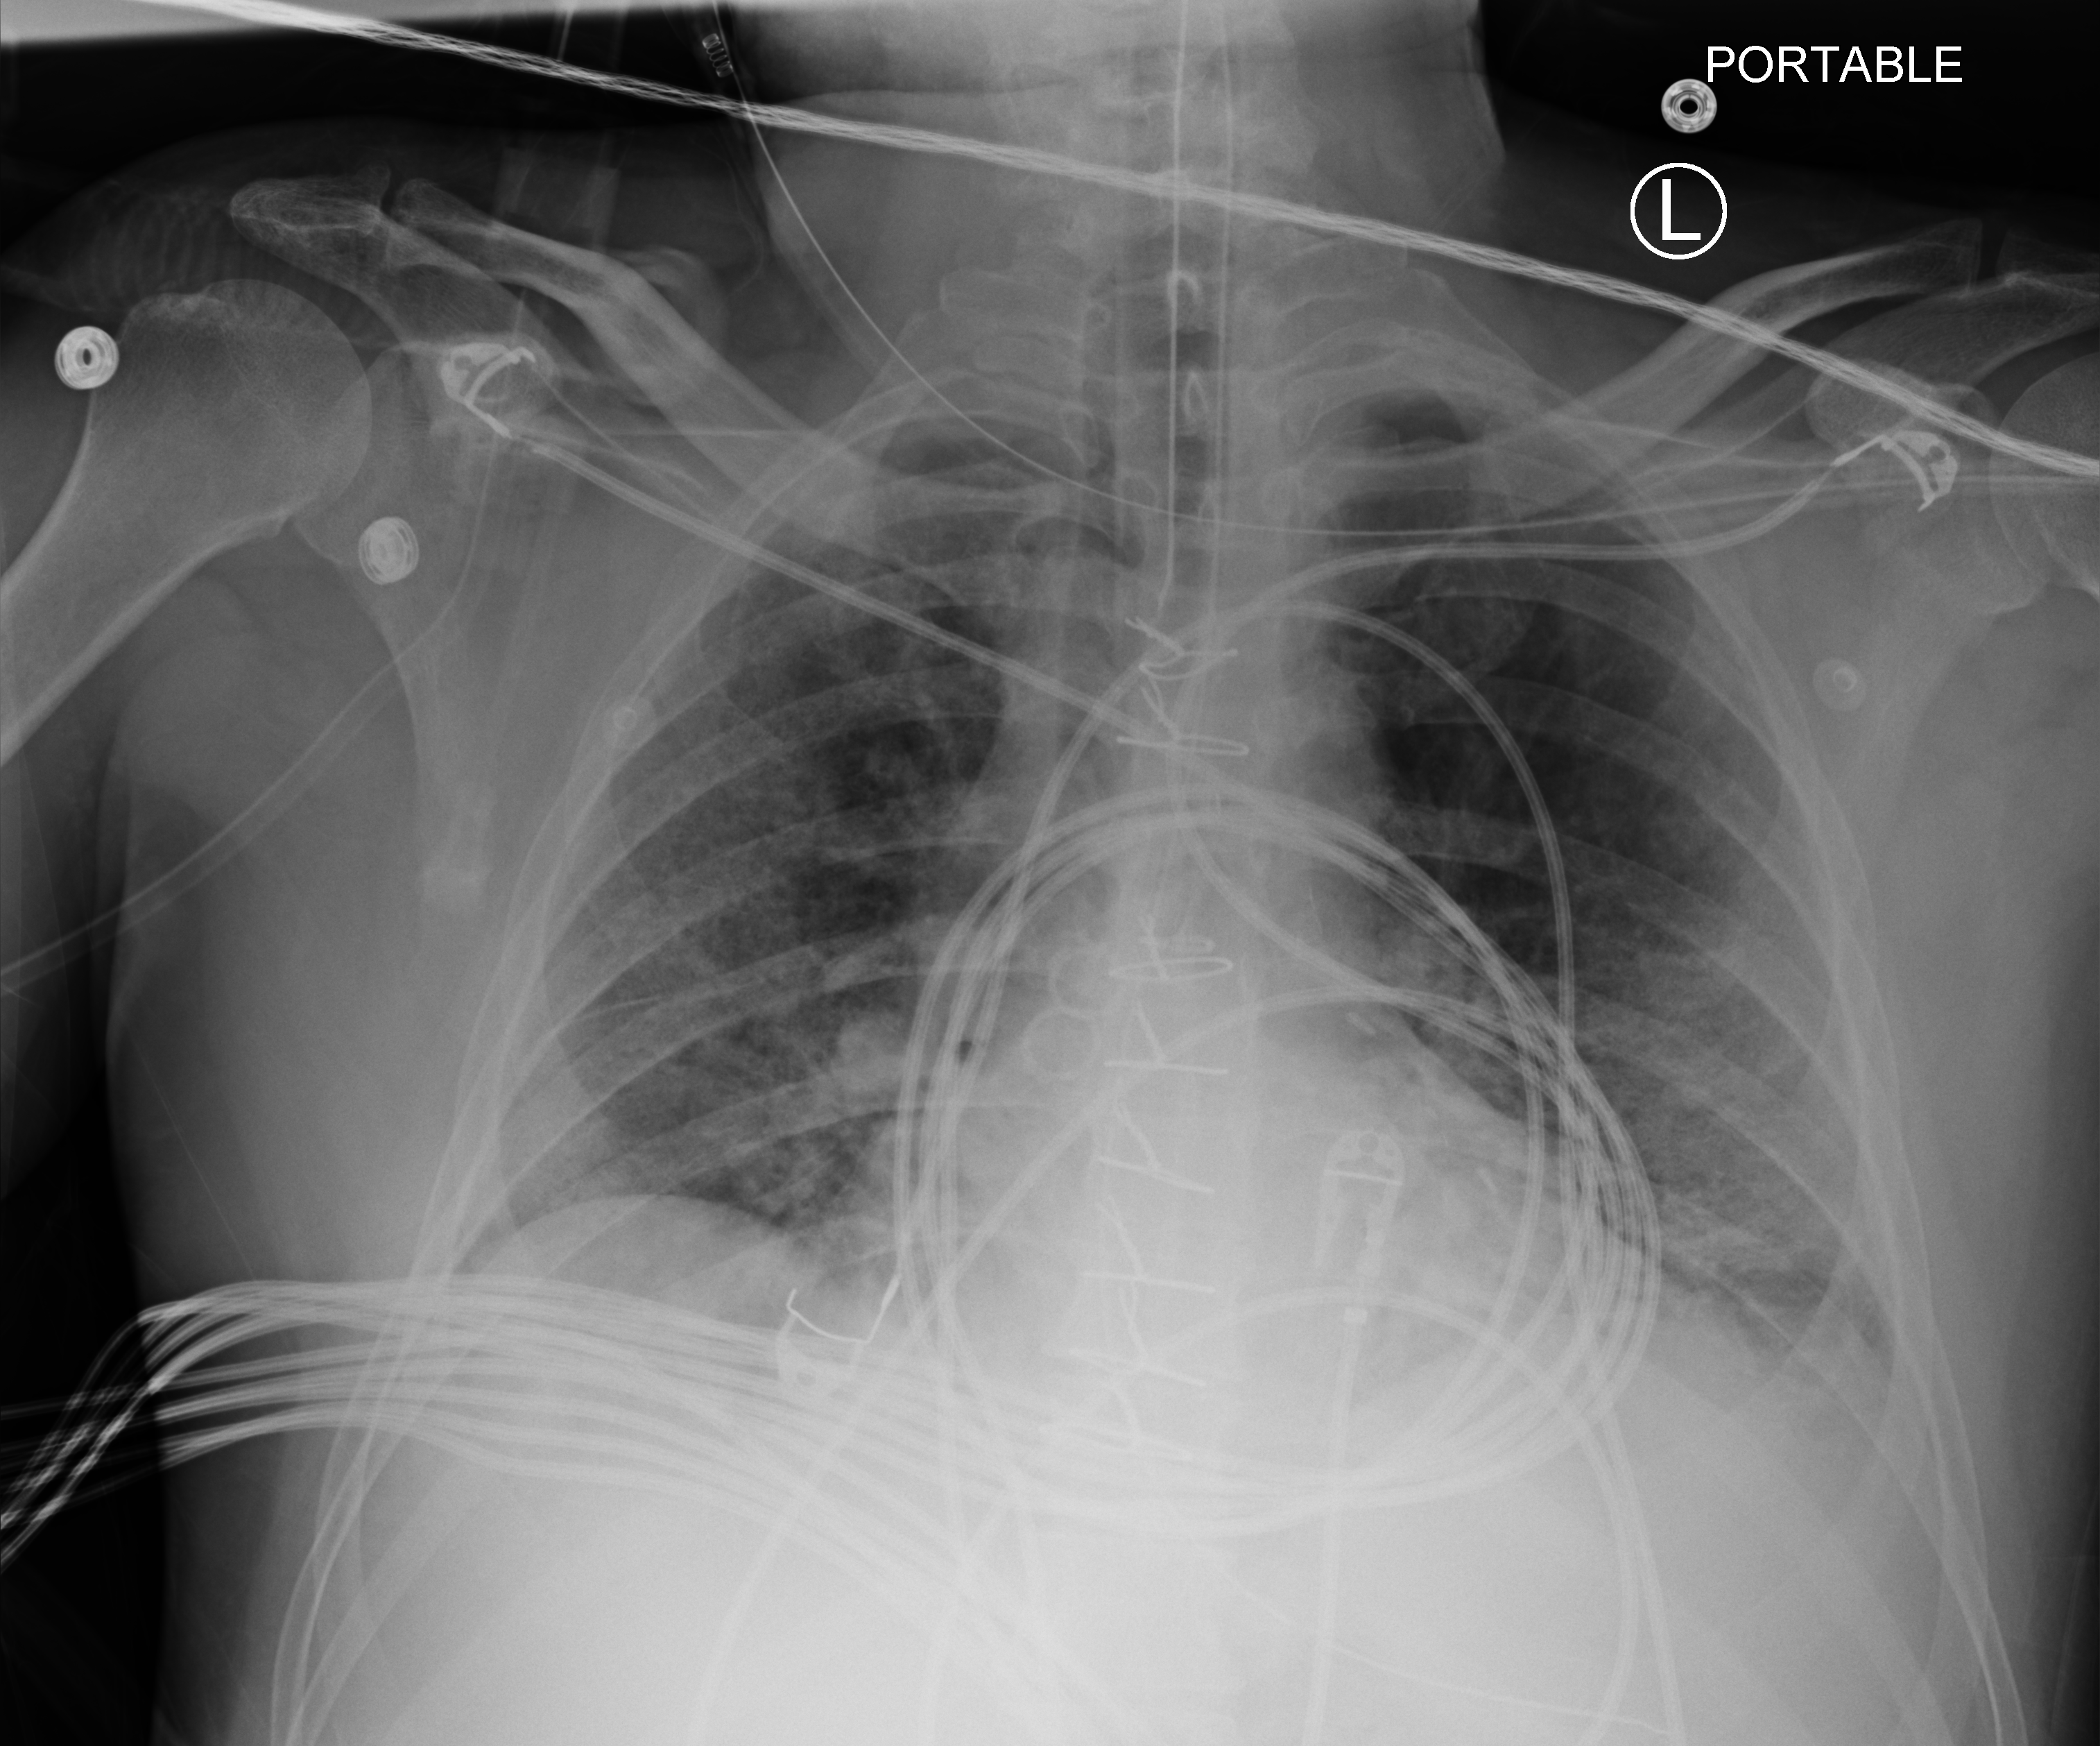
Bedside chest radiograph (computed radiography), anteroposterior (AP) projection. Patient hospitalised with COVID-19; male, aged 18–59 years.
Hospital-stay facts (about this admission, not read from this image; timing relative to this image not recorded):
- mechanically ventilated during this hospital stay: yes
- diabetes (admission record): yes